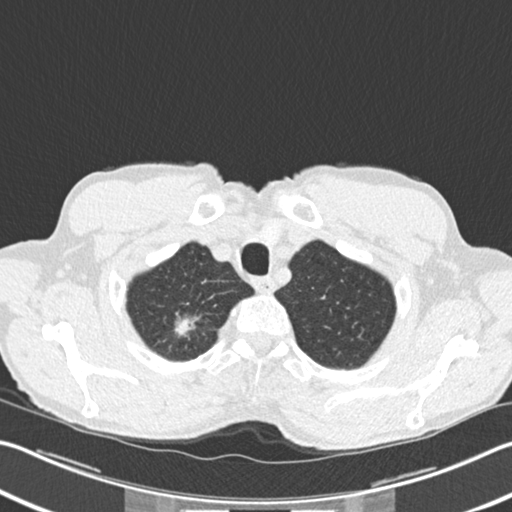
Low-dose screening chest CT, one axial slice; slice 199 of 220 in the series (ordered by position); reconstruction kernel B30f; 120 kVp; lung window (W 1500 / L -600 HU); 2 mm slice thickness; 512 × 512 image matrix, field of view 342 × 342 mm.
Outlined on this slice (expert manual segmentation):
- lesion 1 (tumor, upper lobe of right lung): bounding box [x1, y1, x2, y2] px = [175, 317, 198, 336]